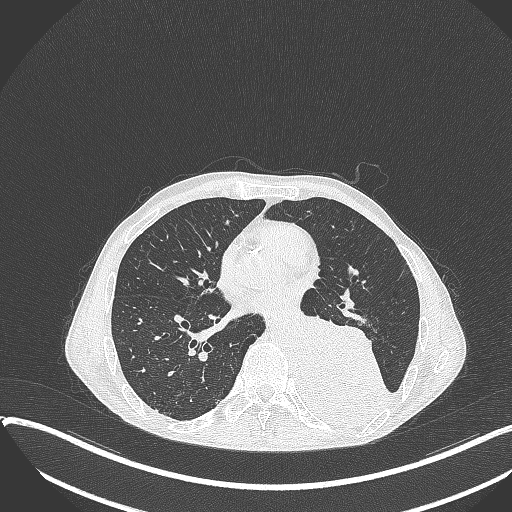
Chest CT, one axial slice; position 163 of 401 along the scan axis; reconstruction kernel B70f; lung window (W 1500 / L -600 HU); 512 × 512 image matrix, field of view 400 × 400 mm. Male patient, age 57 years. Case-level facts recorded for this patient, not image findings: clinical TNM (as recorded): T4 N0 M0.
Outlined on this slice (rectangle marked by the reading radiologist):
- lung tumour (recorded histology: squamous cell carcinoma): bounding box [x1, y1, x2, y2] px = [297, 309, 394, 427]